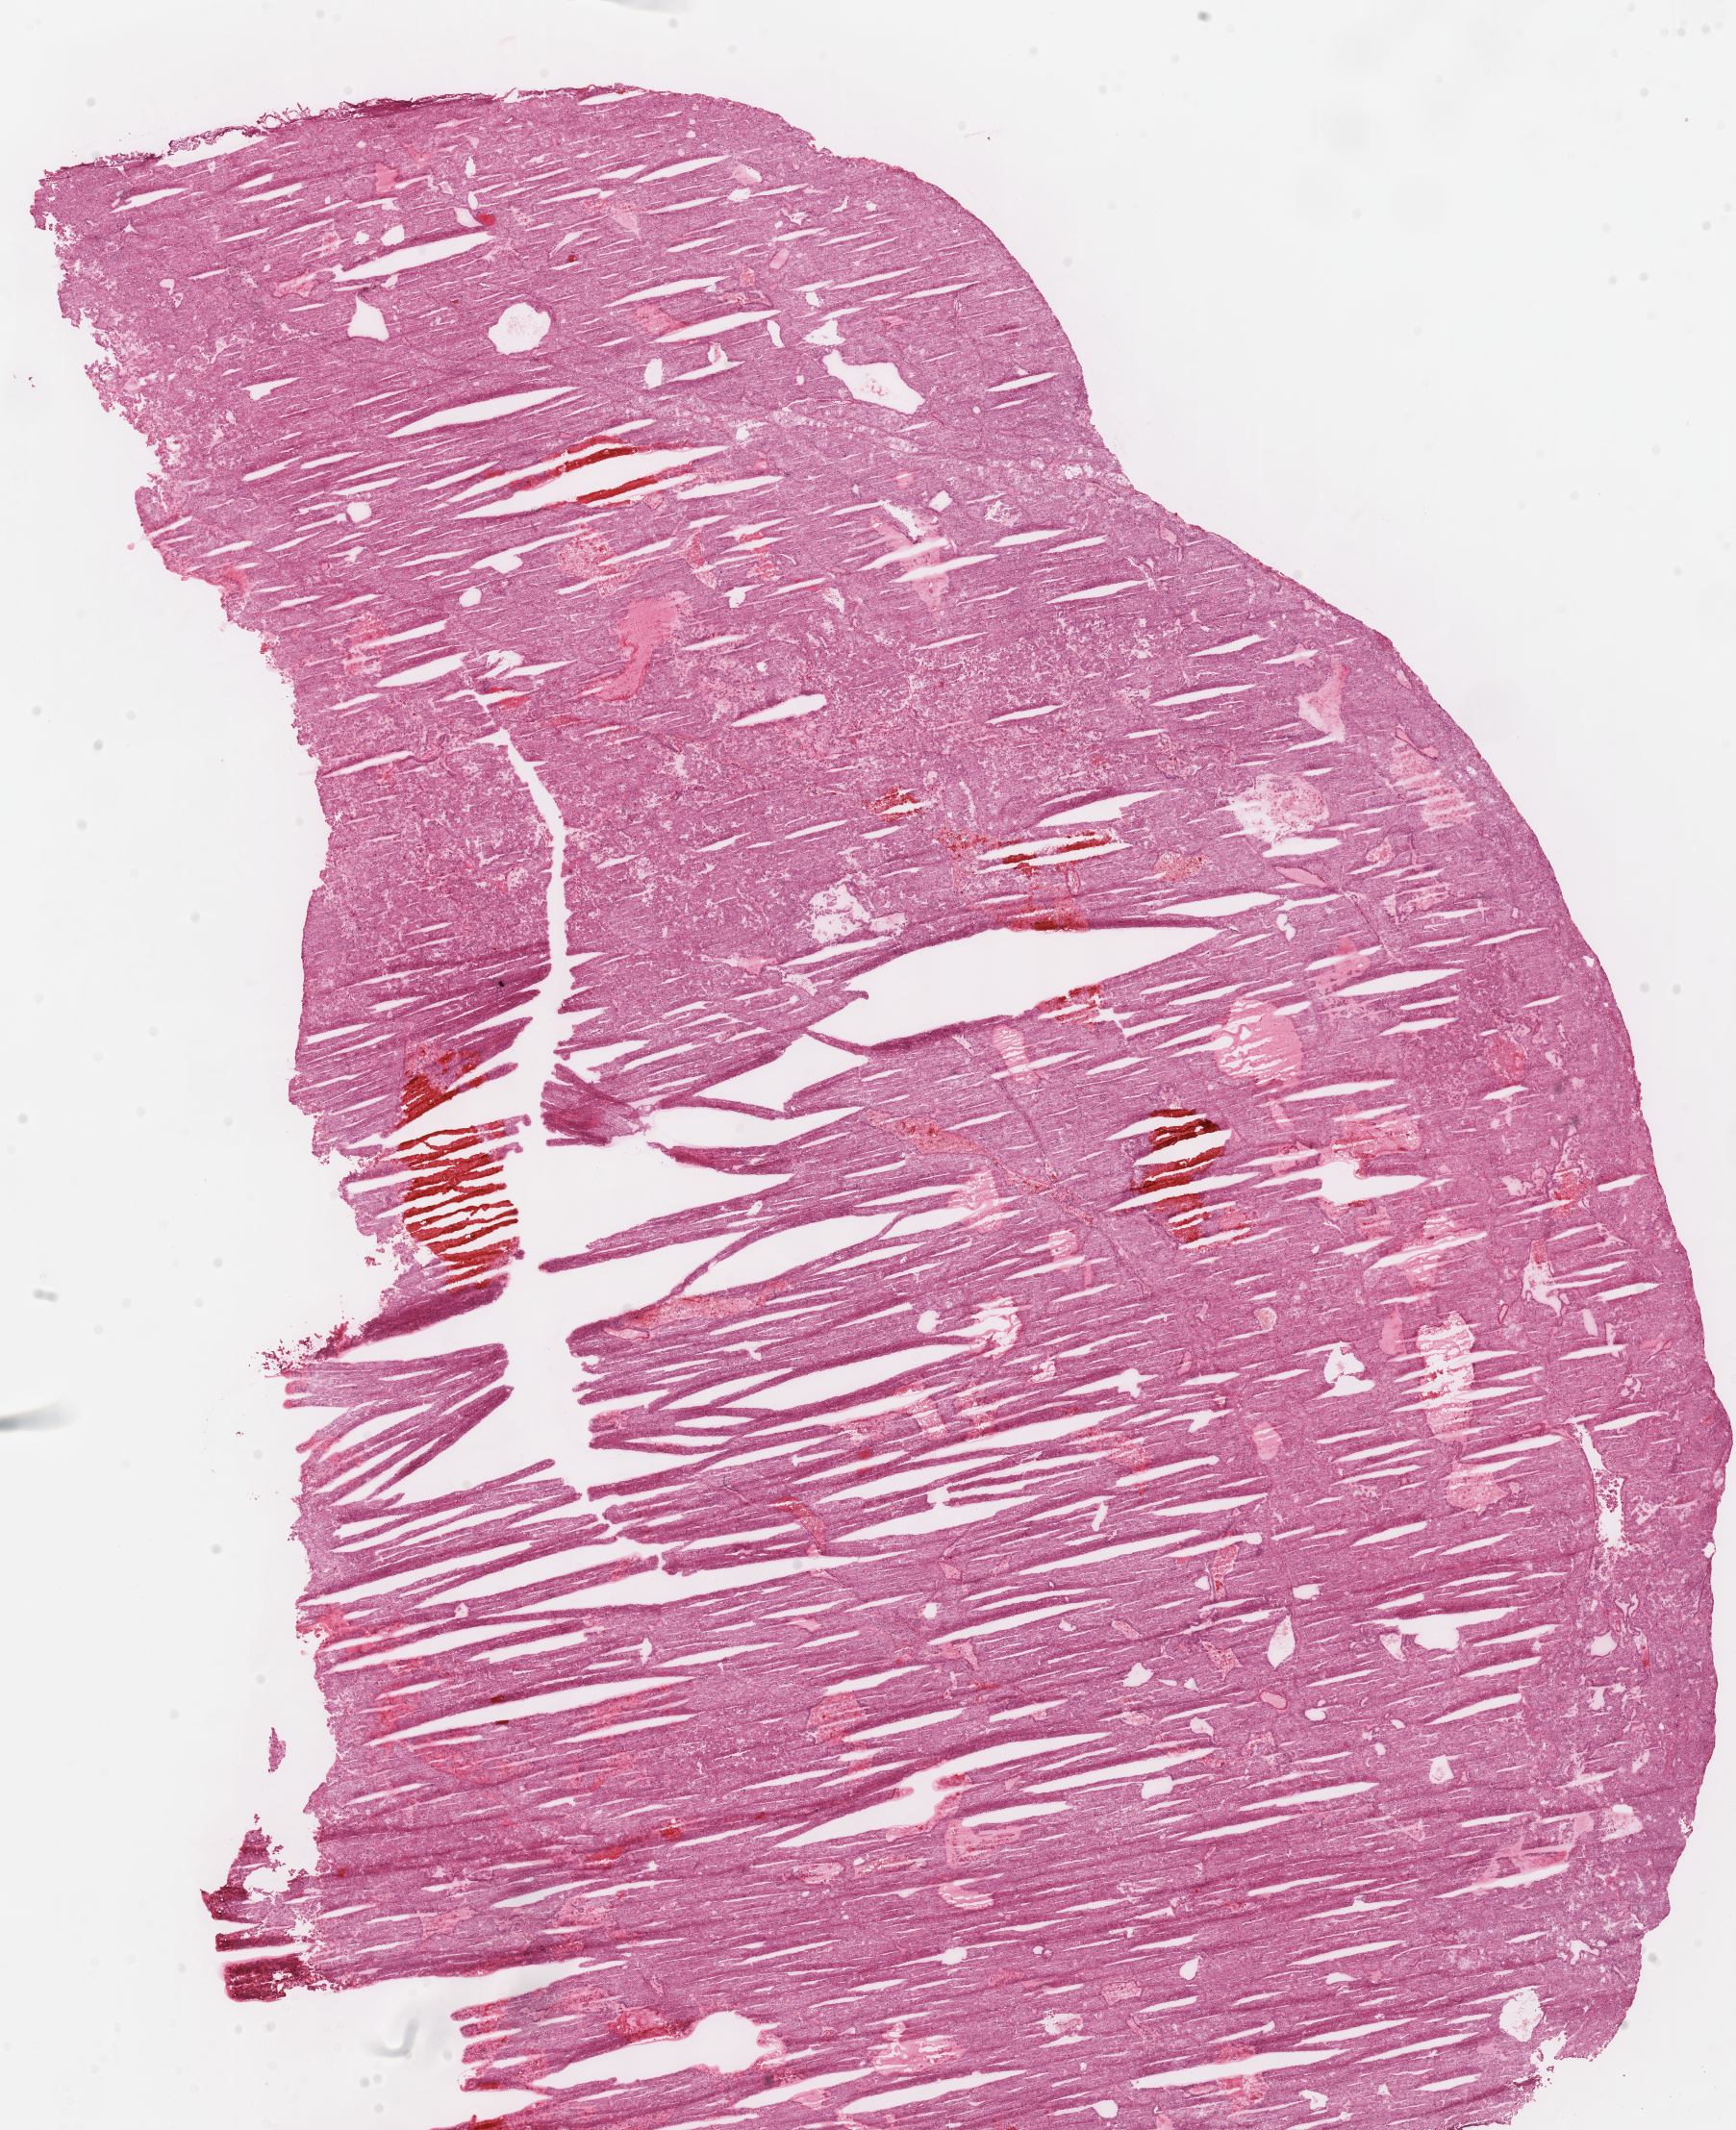
Digitized H&E-stained tissue section (whole slide), shown as a low-resolution overview of the whole scanned area (about 14.2 x 17.4 mm, acquisition: 40x scan), frozen section, primary tumour sample from the kidney. Patient: male, age at initial diagnosis 75 years. Pathologist review of this section (percent, as recorded): tumour cells 90%, tumour nuclei 90%, normal cells 0%, stromal cells 5%, necrosis 5%.
- lymph nodes positive (case pathology): 0 of 13 examined
- histologic diagnosis: Renal cell carcinoma, chromophobe type
- AJCC pathologic stage: III (6th edition)